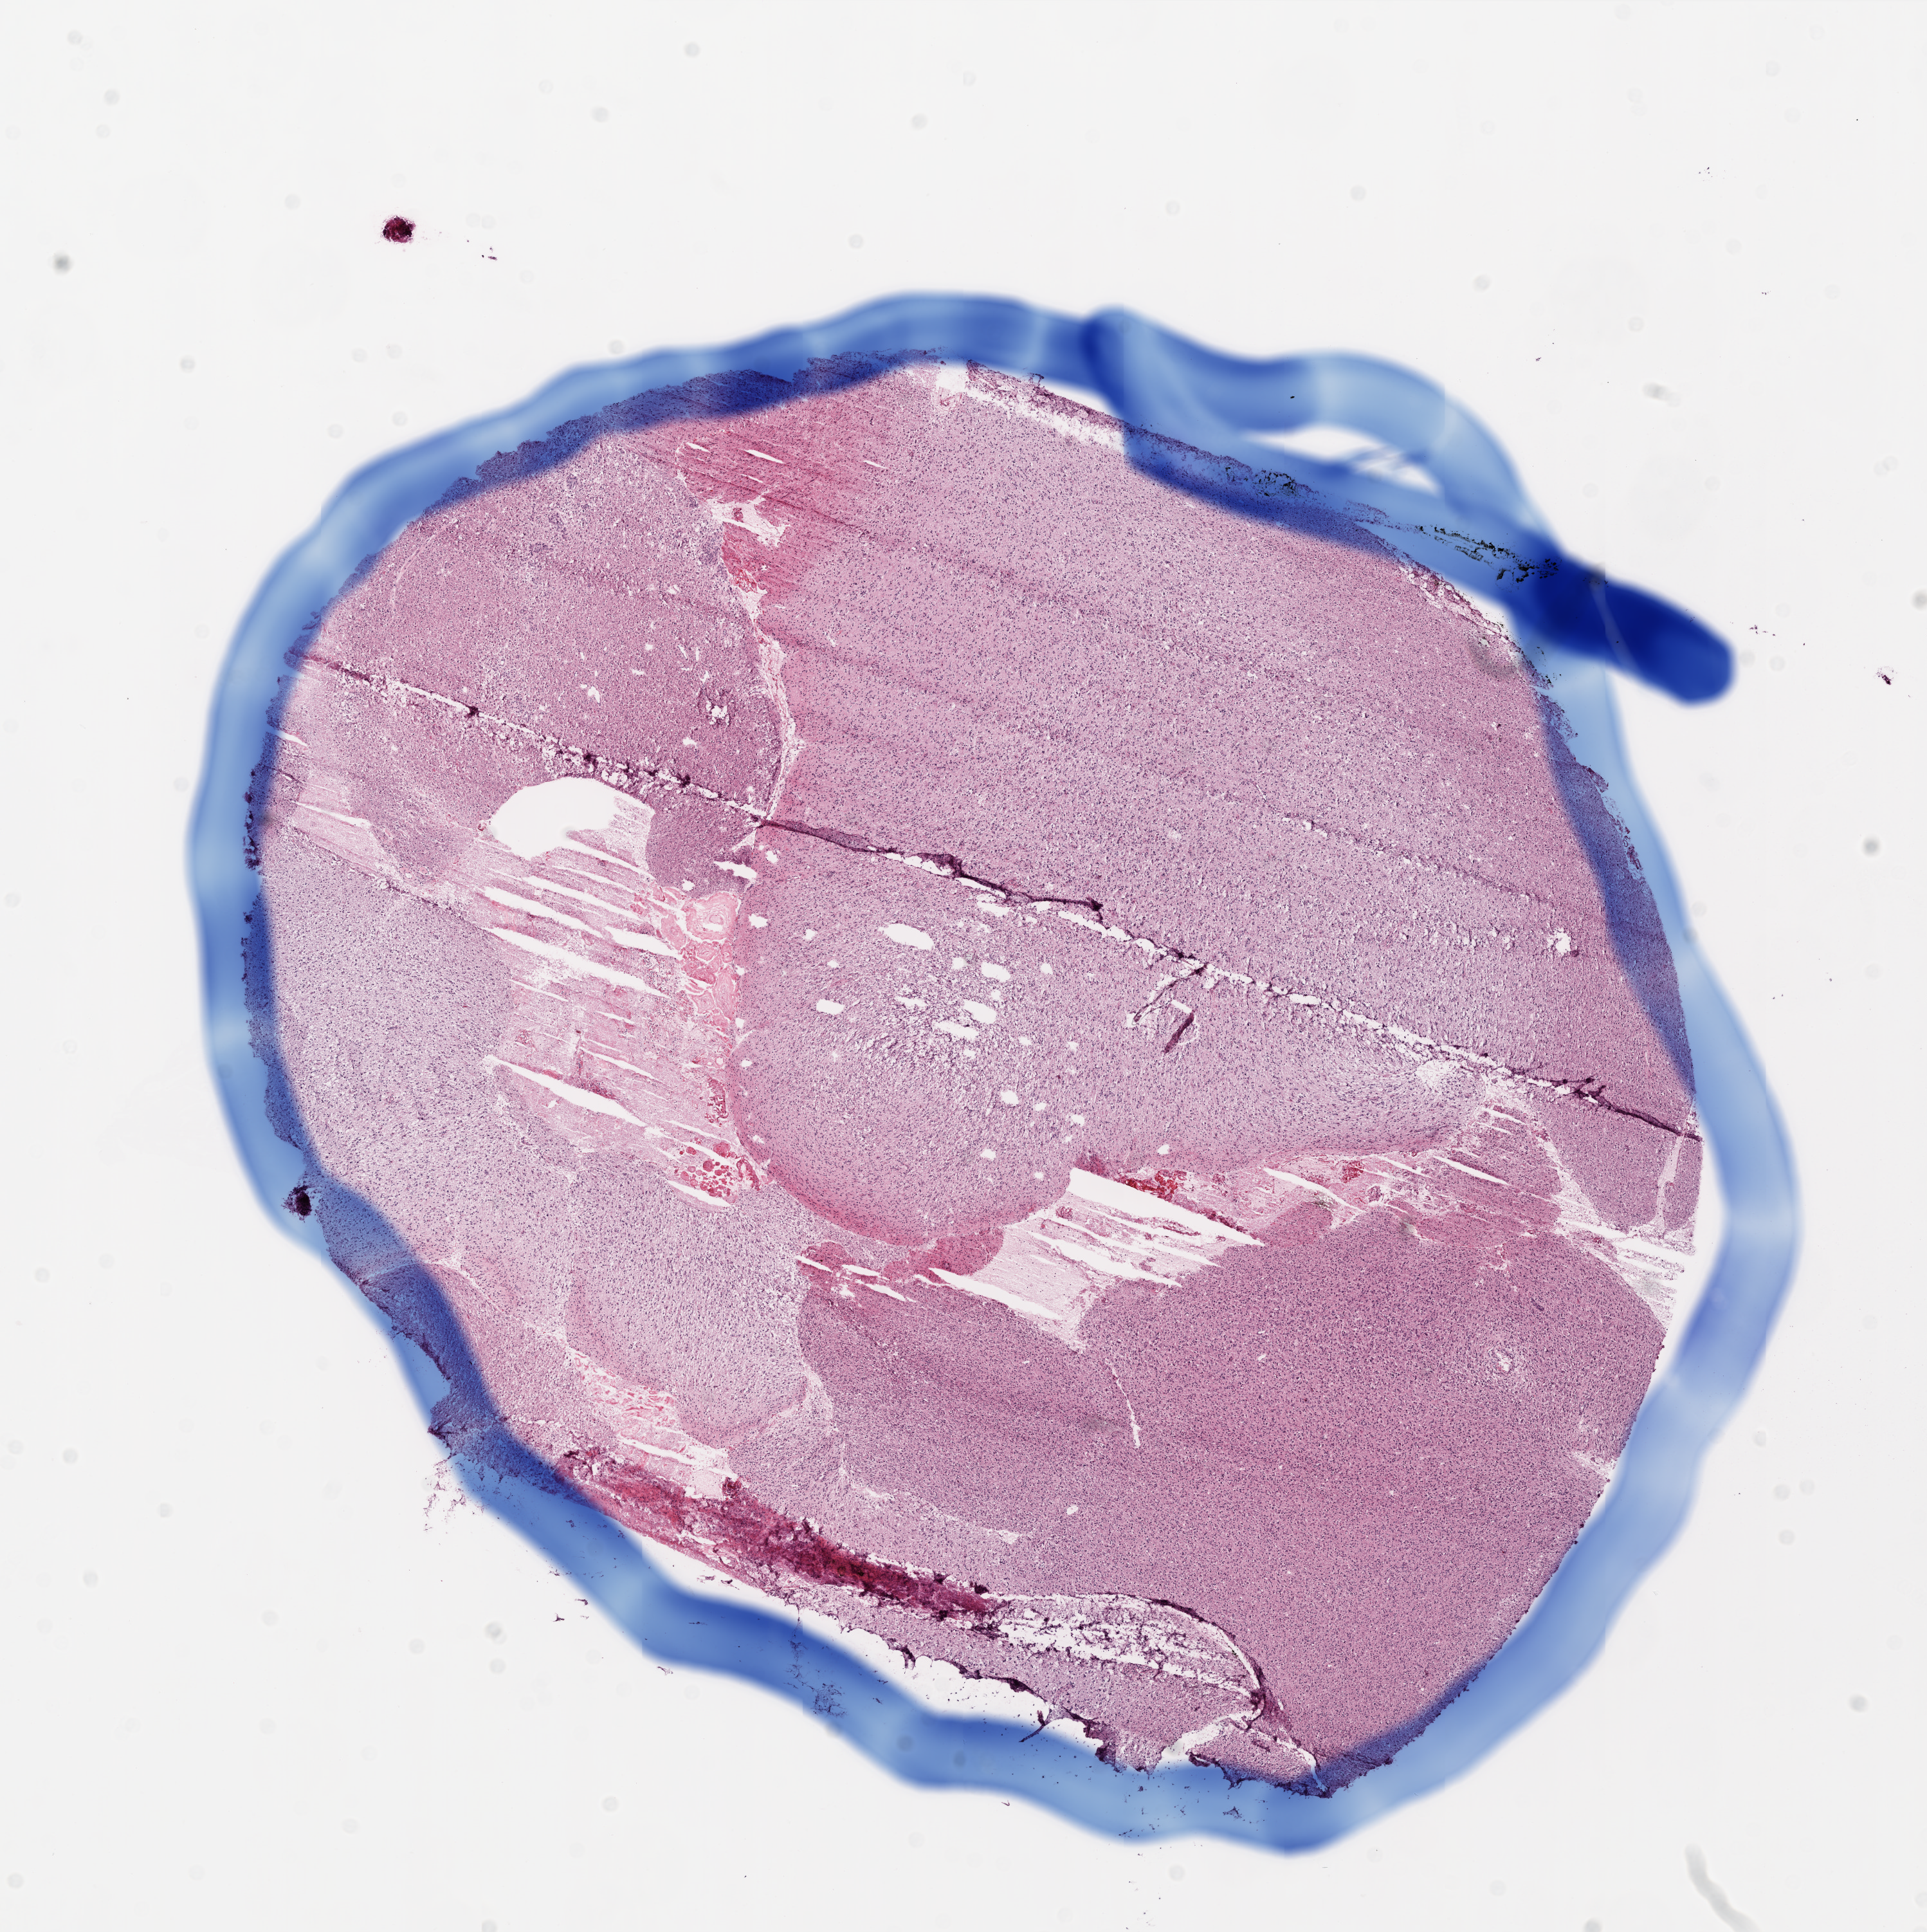
Digitized Hematoxylin and eosin (H&E) stained tissue section (whole slide) — low-resolution overview of the scanned area, about 12.0 x 12.0 mm (from a 20x scan); frozen section; sample: primary tumour, brain. Male, age 67 years at initial diagnosis. Pathologist review of this section (percent, as recorded): tumour cells 80%, tumour nuclei 100%, normal cells 15%, stromal cells 0%, necrosis 5%.
Histologic diagnosis: Glioblastoma.